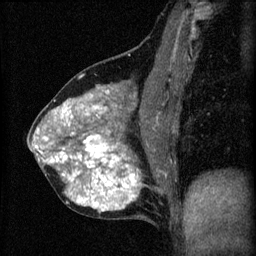
Breast MRI (dynamic contrast-enhanced), one sagittal slice. Slice 29 of 60 in the series (ordered by position). 3 images stored at this slice position (order not interpretable as contrast timing). 1.5 T. TE 4.2 ms, TR 8.2 ms. 2 mm slice thickness. 256 × 256 image matrix, field of view 180 × 180 mm. Female patient, age 40 years.
Annotated regions visible in this slice (semi-automatically segmented with operator editing):
- analysis volume of interest (the breast-tissue region the enhancement analysis was run in; not a lesion): box from (x=28, y=76) to (x=179, y=219) px
- tumour enhancement mask (voxels above the 70 % enhancement threshold inside the analysis volume of interest): (x=36, y=94)–(x=143, y=211)